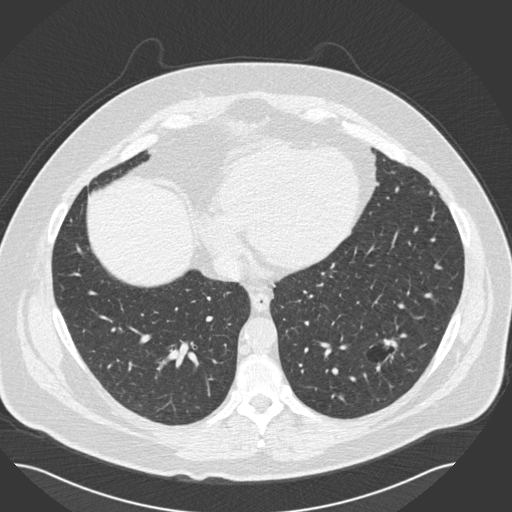
Axial slice from a low-dose chest CT screening exam, second annual screen, lung window (W 1500 / L -600 HU), 2 mm slice thickness, slice 95 of 162 in the series, 512 × 512 image matrix. Male, age 57 years at enrolment. Current smoker at enrolment.
Lesion marked by an expert reader, bounding box (x1, y1, x2, y2) in pixels: (357, 323, 423, 381). Screening reader's record for this exam (one nodule recorded; not confirmed to be the boxed lesion): non-calcified nodule or mass ≥4 mm, left lower lobe, 19 × 15 mm, pre-existing on the prior screen: yes; interval growth: no. Lung cancer was diagnosed 434 days after this screen: squamous cell carcinoma, NOS, left lower lobe, moderately differentiated (G2), stage IA (AJCC 6th edition), 22 mm at pathology.